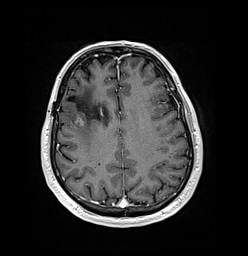
Brain MRI from a brain-tumour surgery series, one axial slice. Position 58 of 176 along the scan axis. T1-weighted post-contrast. 248 × 256 image matrix, field of view 242 × 250 mm. From the clinical record (not read from this slice): histopathology: Oligodendroglioma; WHO grade: 3; IDH mutation: yes.
Structures marked on this image (outlined manually by an expert reader):
- previous resection cavity: box from (x=67, y=97) to (x=77, y=102) px
- tumour: (x=73, y=113)–(x=86, y=127)